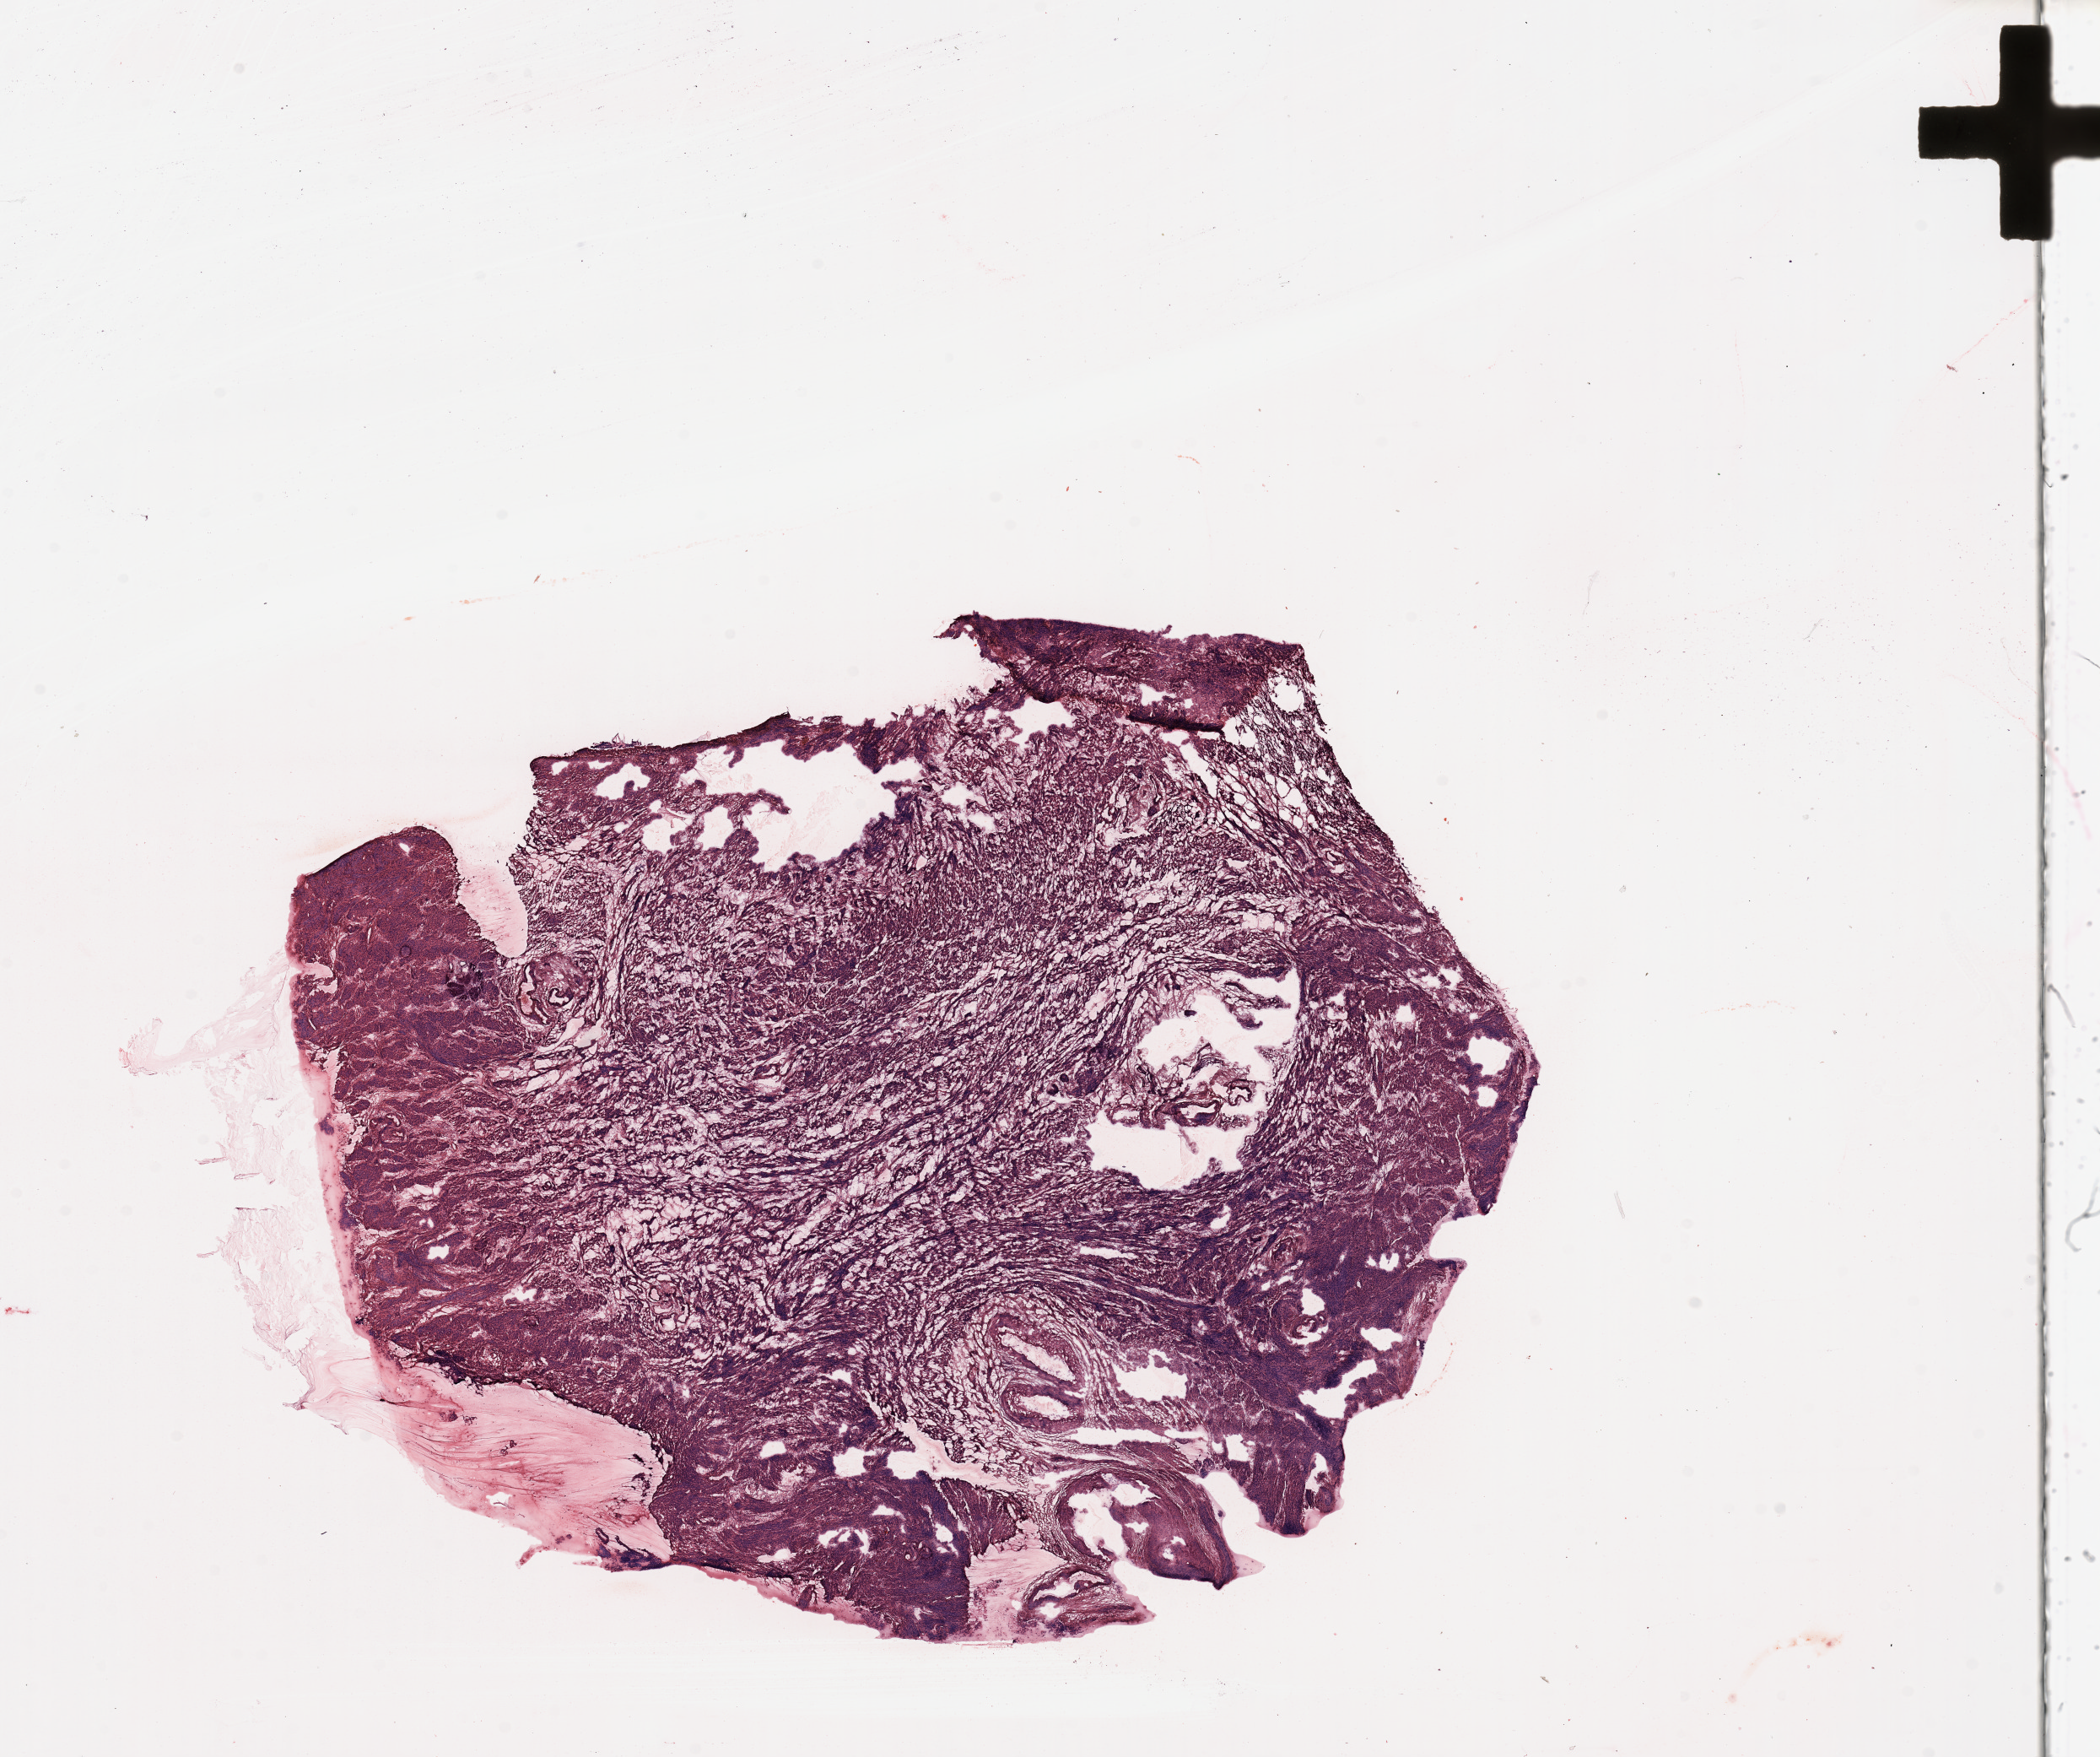
Whole-slide histology image, H&E — low-resolution overview of the scanned area, about 19.7 x 16.5 mm; uterus, normal (non-tumour) tissue. Female, 68 y/o.
This section: normal (non-tumour) tissue from the same patient. Patient diagnosis: Endometrioid adenocarcinoma, NOS.